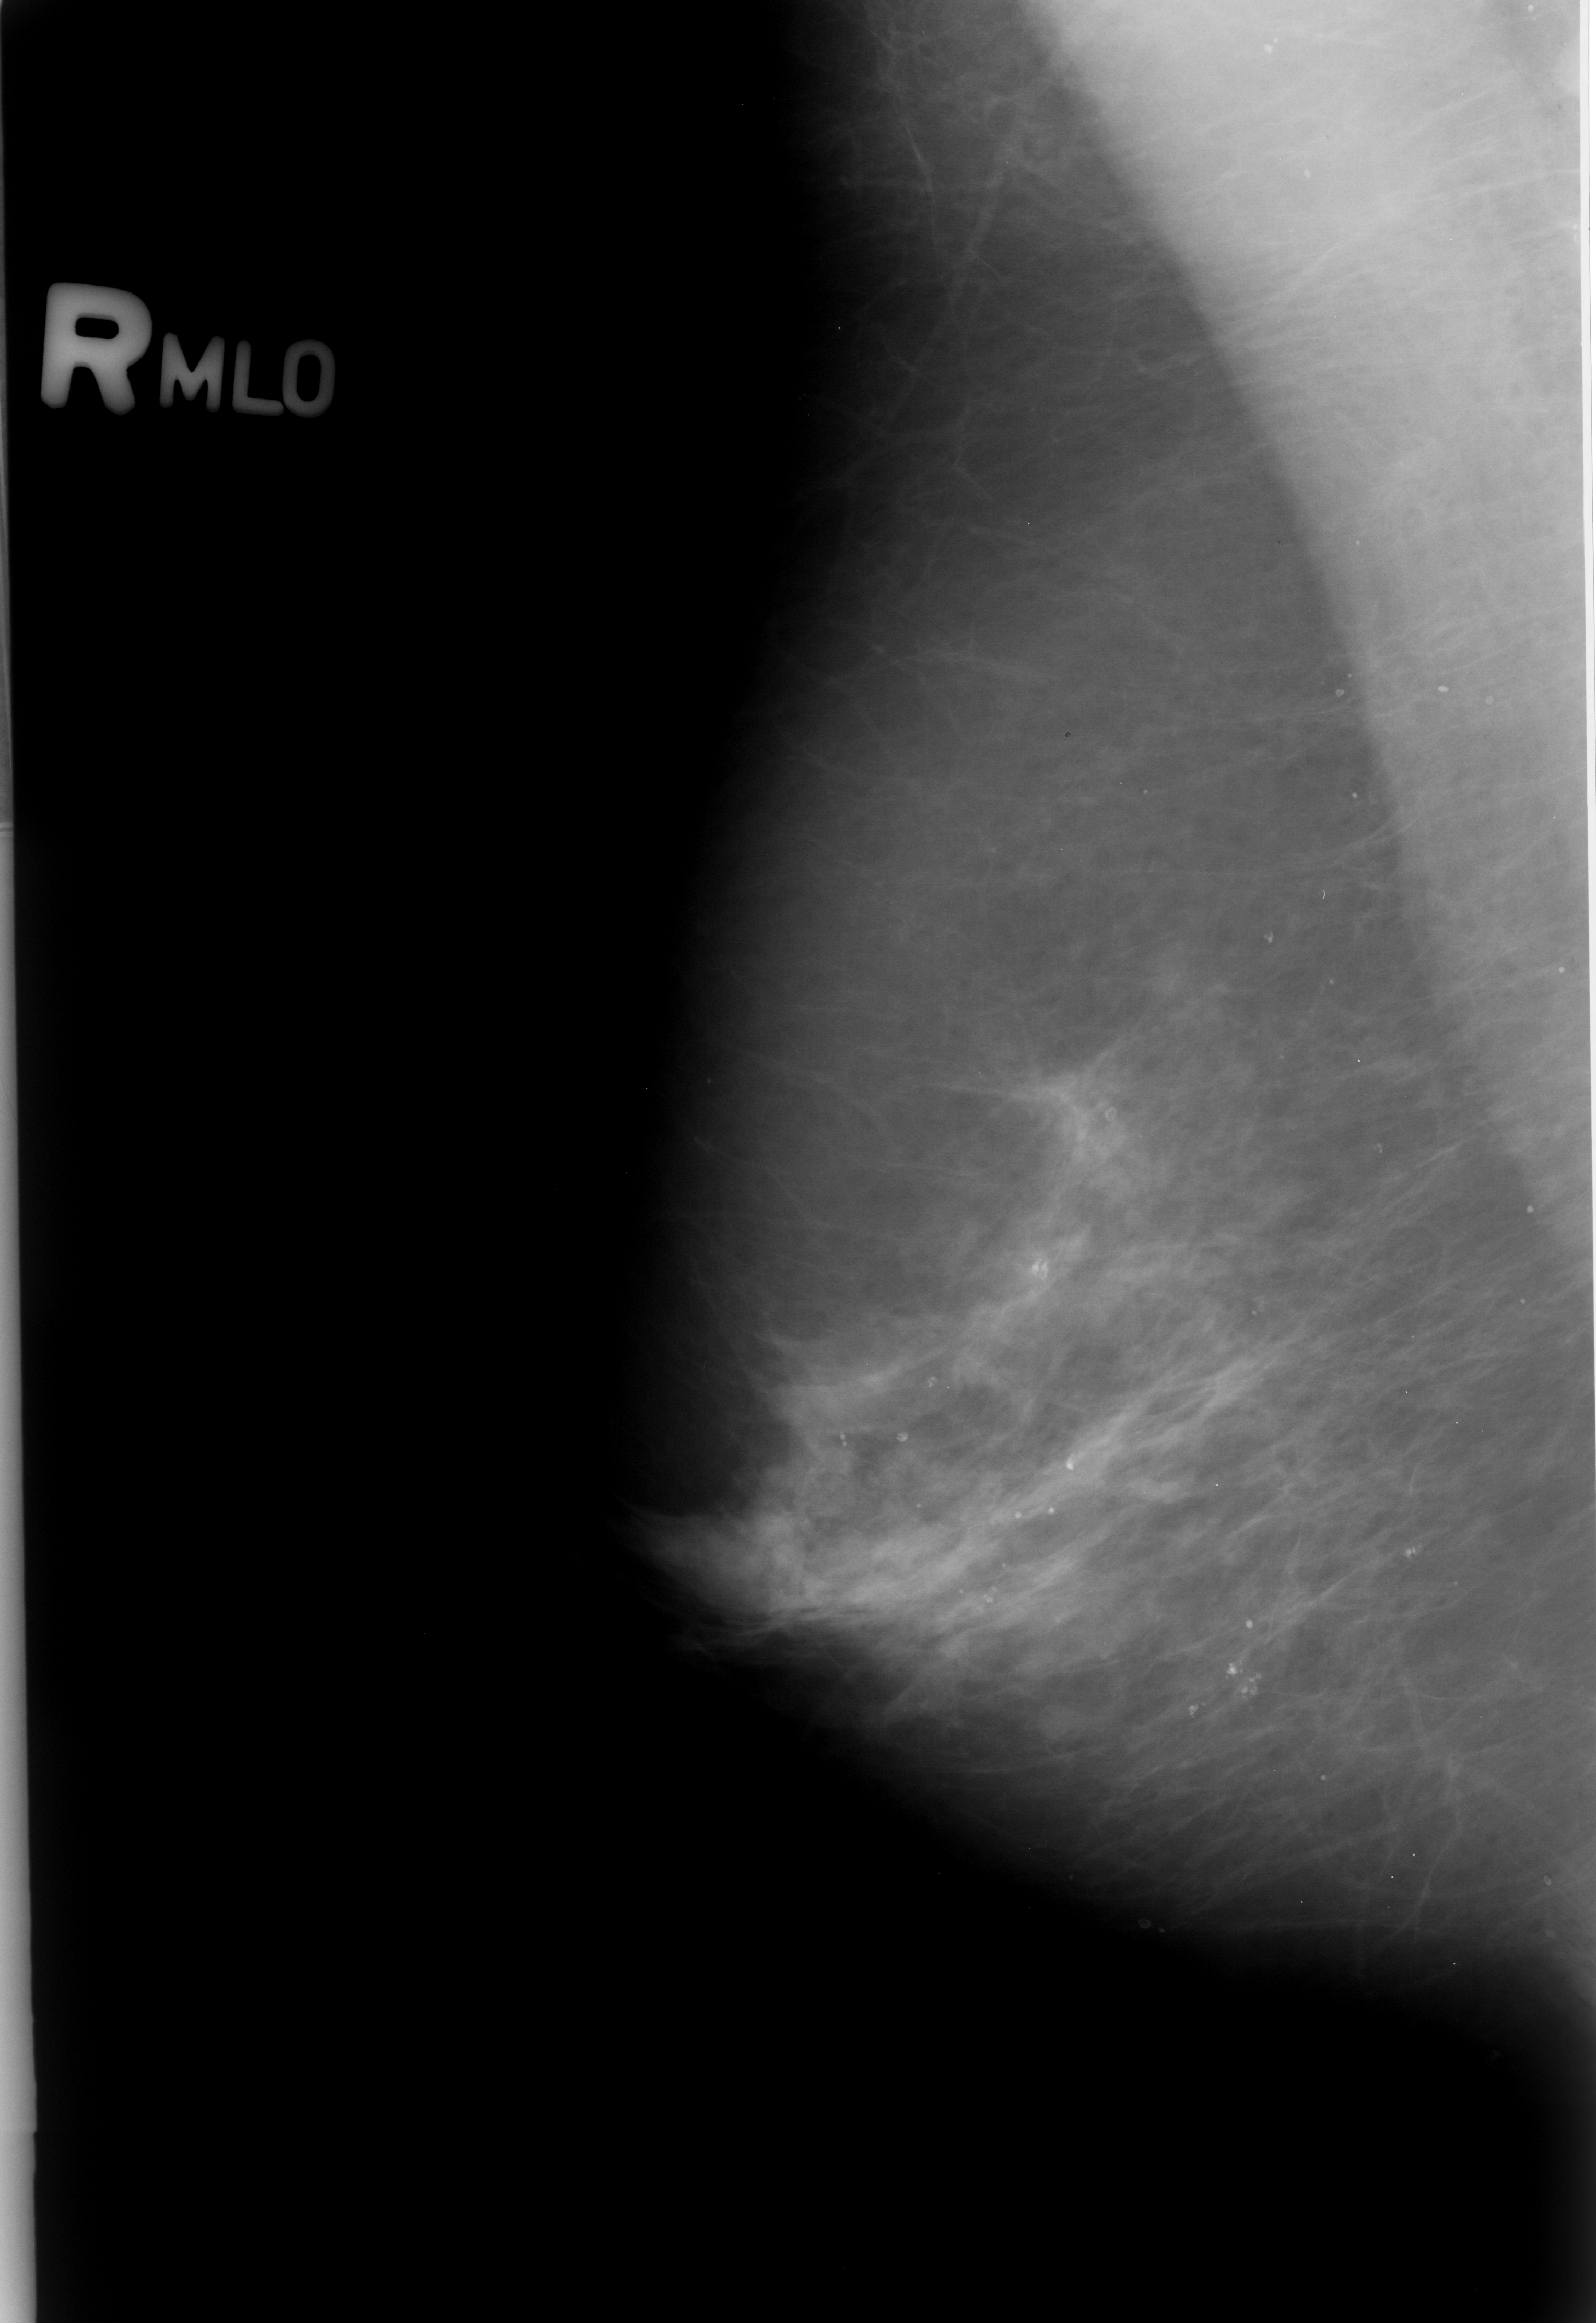
Mammogram (digitized film); right breast; MLO view; BI-RADS breast density category 2 (scale 1–4).
Marked findings (only marked abnormalities are described; nothing is implied about the rest of the image): Finding 1 of 3: calcifications, morphology pleomorphic, distribution clustered; BI-RADS assessment category 2; benign without callback (not worked up further). Finding 2 of 3: calcifications, morphology pleomorphic, distribution clustered; BI-RADS assessment category 2; benign; no additional work-up was recommended (benign without callback). Finding 3 of 3: calcifications, morphology pleomorphic, distribution clustered; BI-RADS assessment category 2; benign; no additional work-up was recommended (benign without callback).